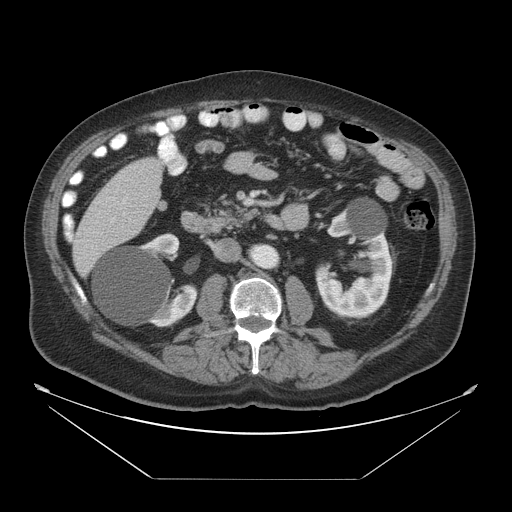
Contrast-enhanced abdominal CT, one axial slice. Slice 16 of 45 in the series (ordered by position). Intravenous contrast given. Soft-tissue window (W 400 / L 40 HU). 5 mm slice thickness. 512 × 512 image matrix, field of view 463 × 463 mm. Male patient, age 87 years. Case-level facts recorded for this patient, not image findings: diagnosis: colorectal cancer liver metastases, imaged before liver resection; multiple liver metastases: no; largest metastasis: 4.5 cm; disease in both lobes: yes.
Outlined on this slice (manually delineated by an expert):
- liver: bounding box (x1, y1, x2, y2) in pixels: (72, 158, 165, 278)
- portal vein (with intrahepatic branches): (123, 212, 126, 215)